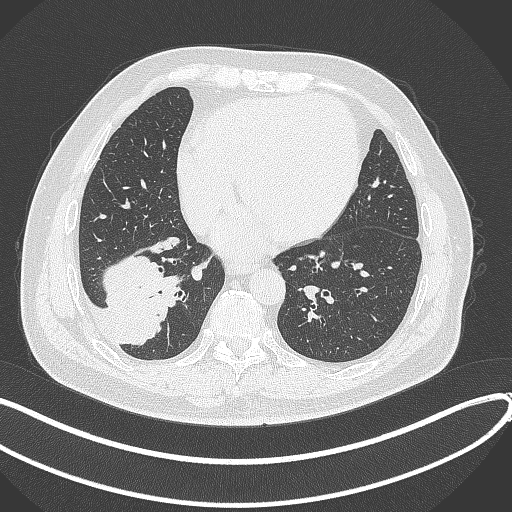
Chest CT, one axial slice. Slice 124 of 360 in the series (ordered by position). Reconstruction kernel B70f. Lung window (W 1500 / L -600 HU). 1 mm slice thickness. 512 × 512 image matrix, field of view 400 × 400 mm. Patient: male, 59 years.
Outlined on this slice (bounding box drawn by a radiologist):
- lung tumour (recorded histology: adenocarcinoma): bounding box [x1, y1, x2, y2] px = [100, 255, 186, 348]